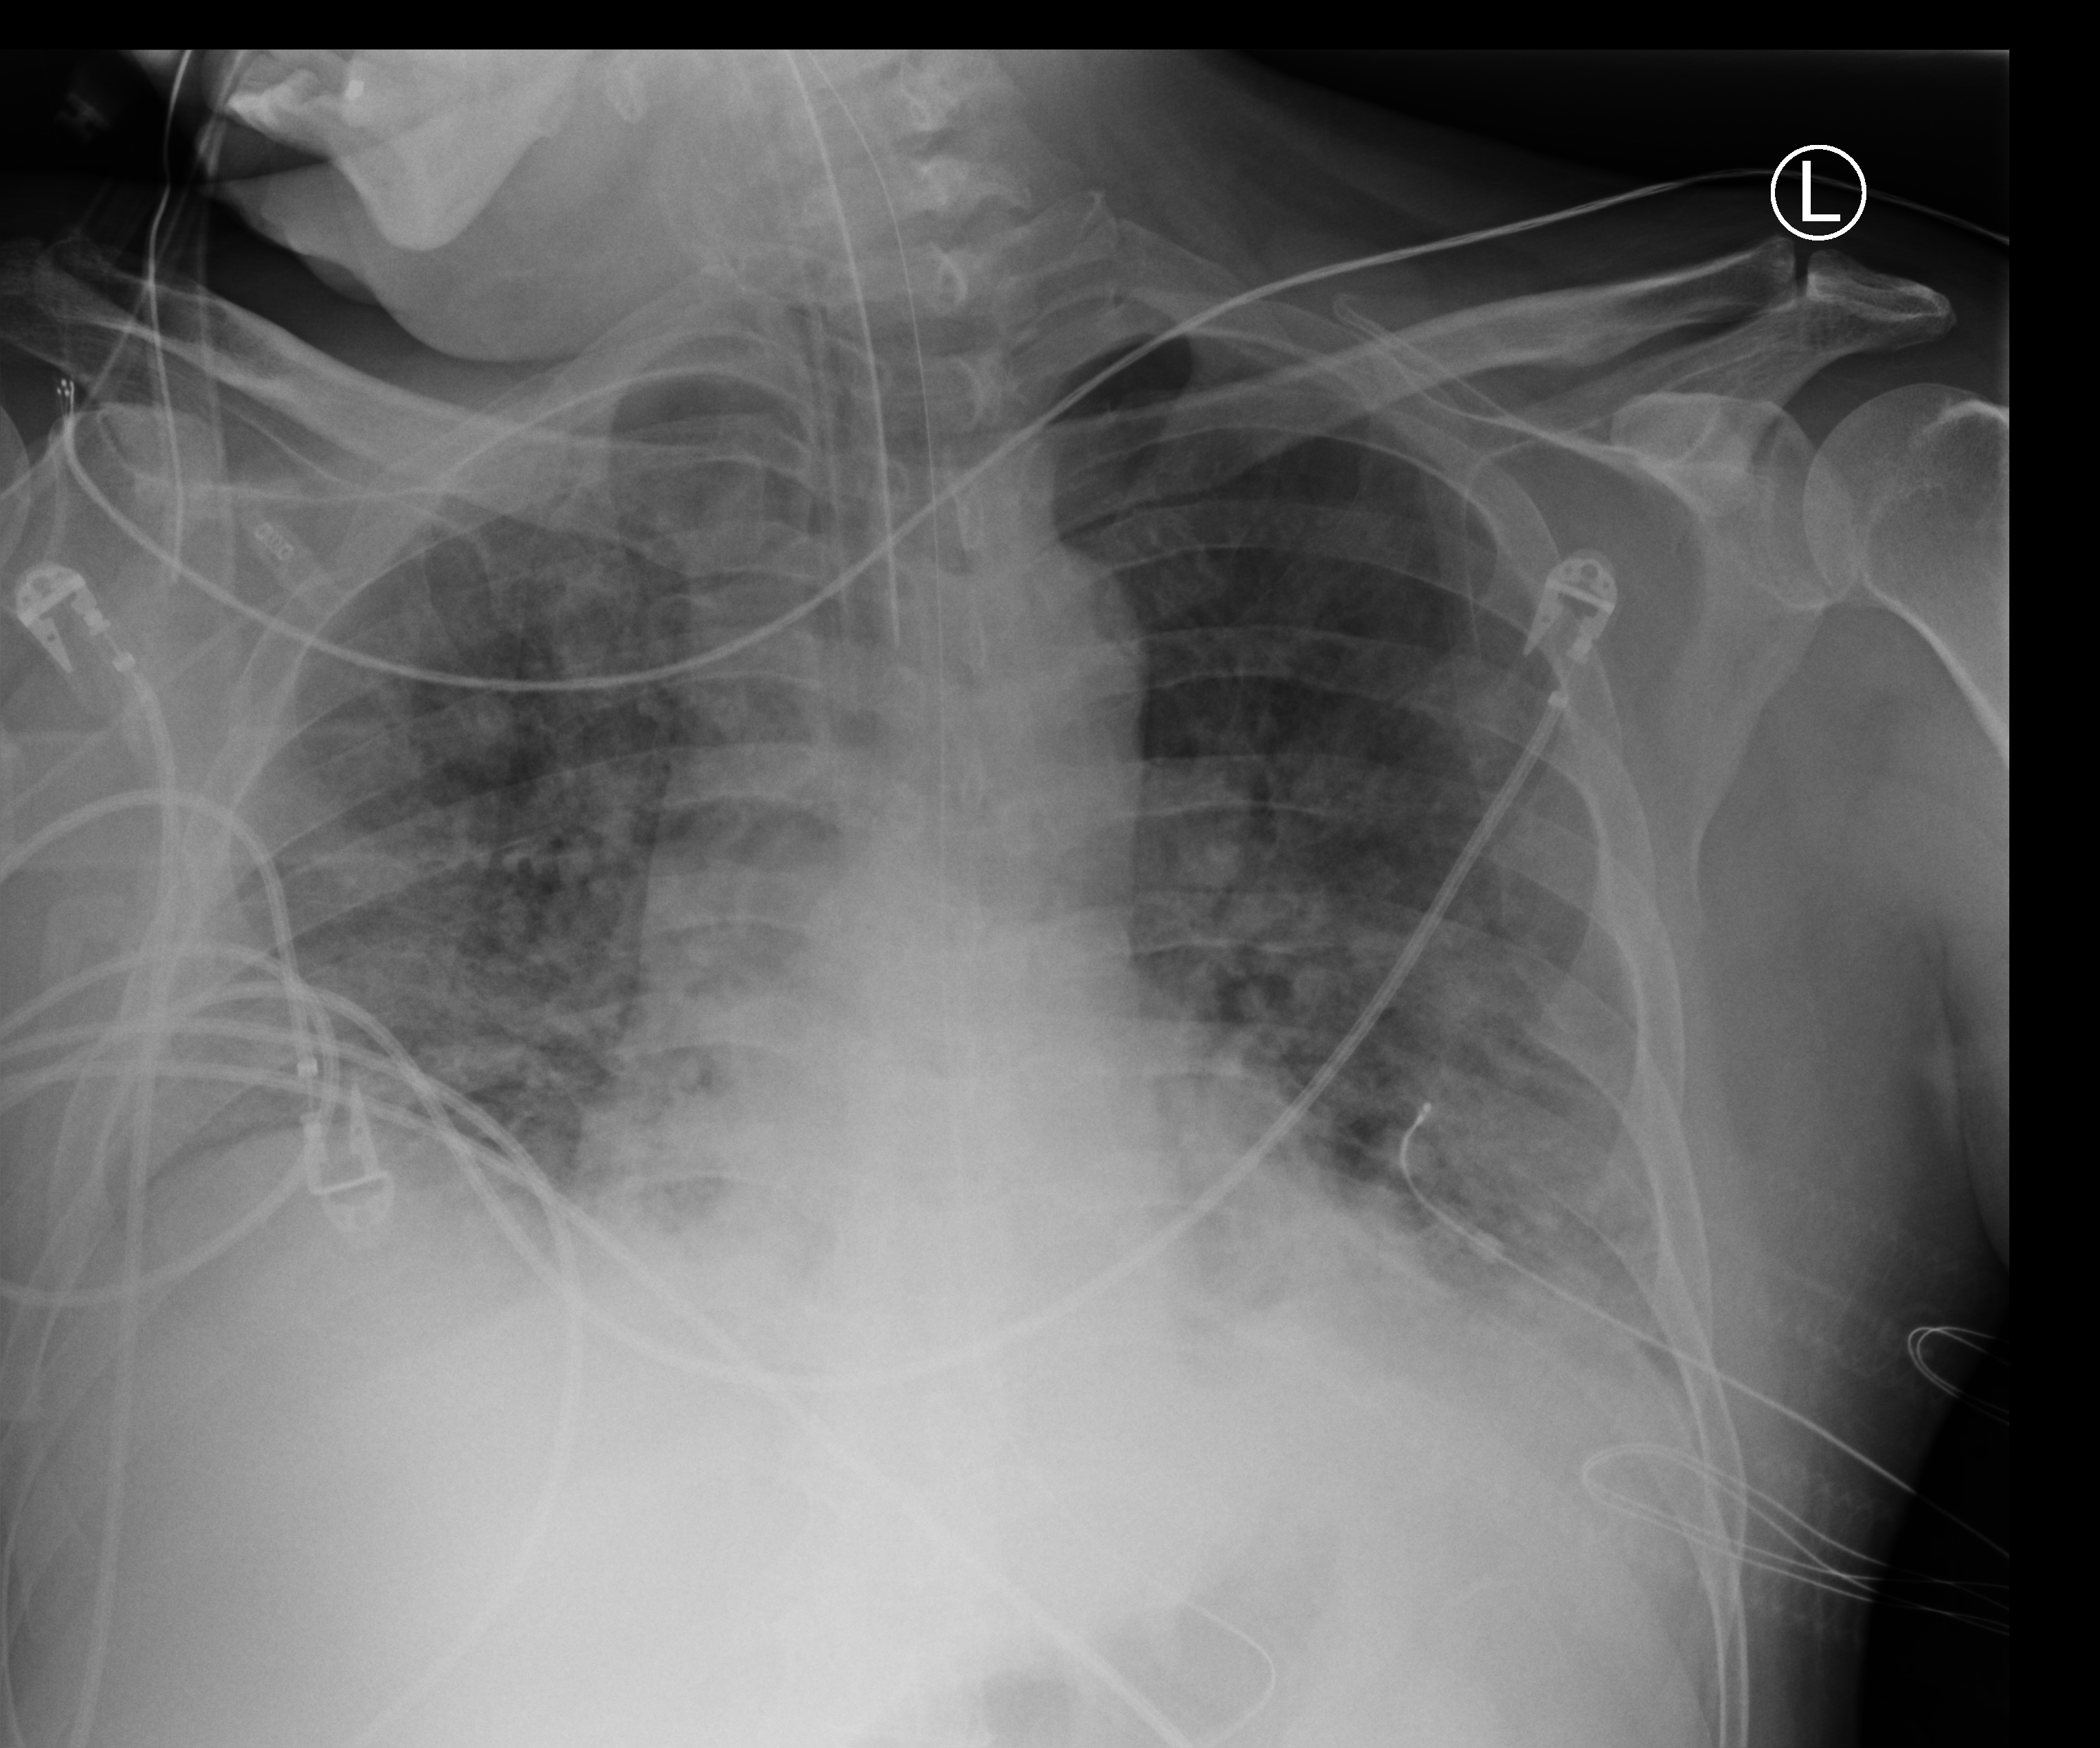
Chest X-ray (portable); anteroposterior (AP) projection. Patient hospitalised with COVID-19; male, aged 18–59 years.
Admission-level facts for this patient (not findings on this image; timing relative to this image not recorded):
- other chronic lung disease (admission record): no
- hypertension (admission record): yes